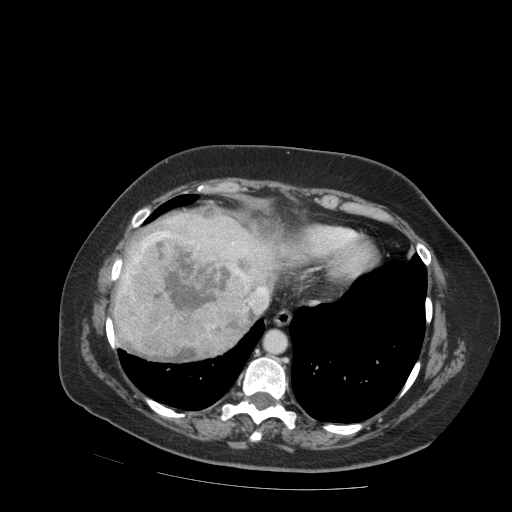
Contrast-enhanced abdominal CT (liver protocol), one axial slice; slice 76 of 99 in the series (ordered by position); reconstruction kernel STANDARD; 140 kVp; soft-tissue window (W 400 / L 40 HU); 512 × 512 image matrix, field of view 400 × 400 mm. From the clinical record (not read from this slice): diagnosis: hepatocellular carcinoma (patient treated with transarterial chemoembolisation; whether this scan precedes or follows treatment is not stated here); TNM stage (as recorded): Stage-IVB; Child-Pugh class: A.
Annotated regions visible in this slice (semi-automatic segmentation, software-assisted and operator-edited):
- liver parenchyma outside the tumour (the mass and vessels are separate outlines, so this box may not span the whole liver): bounding box [x1, y1, x2, y2] px = [112, 212, 288, 346]
- mass: [112, 232, 259, 362]
- liver vessels: [167, 220, 267, 305]